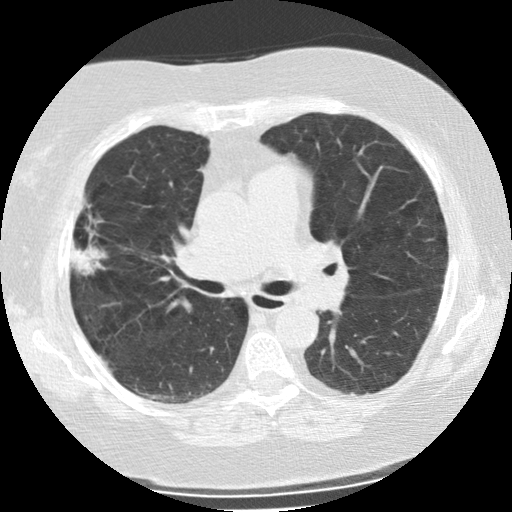
Low-dose screening chest CT, one axial slice. Position 137 of 225 along the scan axis. Reconstruction kernel STANDARD. 120 kVp. Lung window (W 1500 / L -600 HU). 2.5 mm slice thickness. 512 × 512 image matrix, field of view 320 × 320 mm.
Annotated regions visible in this slice (manually delineated by an expert):
- lesion 1 (tumor, upper lobe of right lung): bounding box (x1, y1, x2, y2) in pixels: (70, 245, 106, 276)